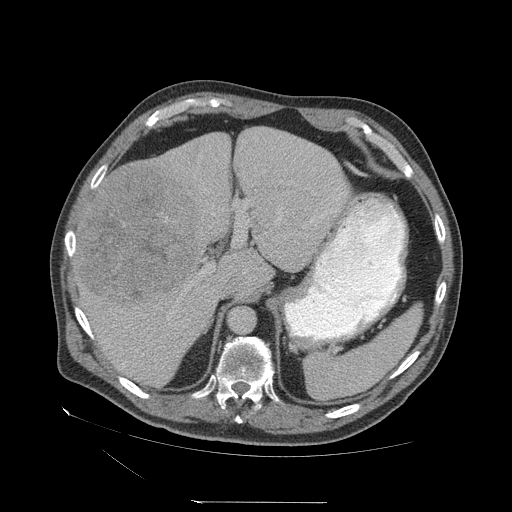
Contrast-enhanced abdominal CT (liver protocol), one axial slice; slice 43 of 83 in the series (ordered by position); reconstruction kernel STANDARD; 140 kVp; soft-tissue window (W 400 / L 40 HU); 512 × 512 image matrix, field of view 460 × 460 mm. From the clinical record (not read from this slice): diagnosis: hepatocellular carcinoma (patient treated with transarterial chemoembolisation; whether this scan precedes or follows treatment is not stated here); TNM stage (as recorded): Stage-I; Child-Pugh class: A; tumour differentiation: well differentiated; tumour nodularity: uninodular.
Annotated regions visible in this slice (semi-automatically segmented with operator editing):
- liver parenchyma outside the tumour (the mass and vessels are separate outlines, so this box may not span the whole liver): bounding box [x1, y1, x2, y2] px = [72, 126, 348, 388]
- mass: [78, 163, 204, 309]
- liver vessels: [86, 211, 336, 338]